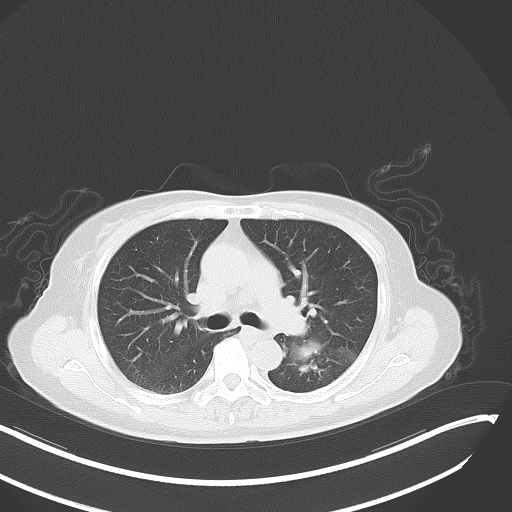
Chest CT, one axial slice; position 25 of 48 along the scan axis; reconstruction kernel B70f; lung window (W 1500 / L -600 HU); 5 mm slice thickness; 512 × 512 image matrix. Patient: female, 64 years. From the clinical record (not read from this slice): clinical TNM (as recorded): T3 N1 M1.
Structures marked on this image (rectangle marked by the reading radiologist):
- lung tumour (recorded histology: small cell carcinoma): box from (x=291, y=341) to (x=322, y=375) px